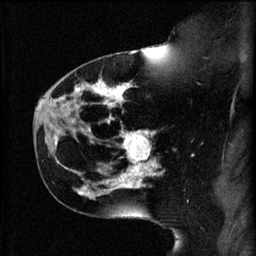
Breast MRI (dynamic contrast-enhanced), one sagittal slice. Slice 38 of 60 in the series (ordered by position). 3 images stored at this slice position (order not interpretable as contrast timing). 1.5 T. TE 4.2 ms, TR 11 ms. 2 mm slice thickness. 256 × 256 image matrix. Female patient, age 44 years.
Annotated regions visible in this slice (semi-automatic segmentation, software-assisted and operator-edited):
- analysis volume of interest (the breast-tissue region the enhancement analysis was run in; not a lesion): bounding box <110,132,161,179> (left, top, right, bottom; pixels)
- tumour enhancement mask (voxels above the 70 % enhancement threshold inside the analysis volume of interest): <118,132,159,179>